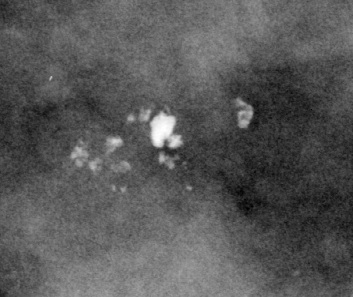
Region of interest cut from a scanned film mammogram (one marked finding); left breast; MLO view.
Calcifications, morphology pleomorphic, distribution clustered; BI-RADS assessment category 4; subtlety rating 5 on a 1 (subtle) to 5 (obvious) scale; pathology result (as recorded, not read from the image): benign.